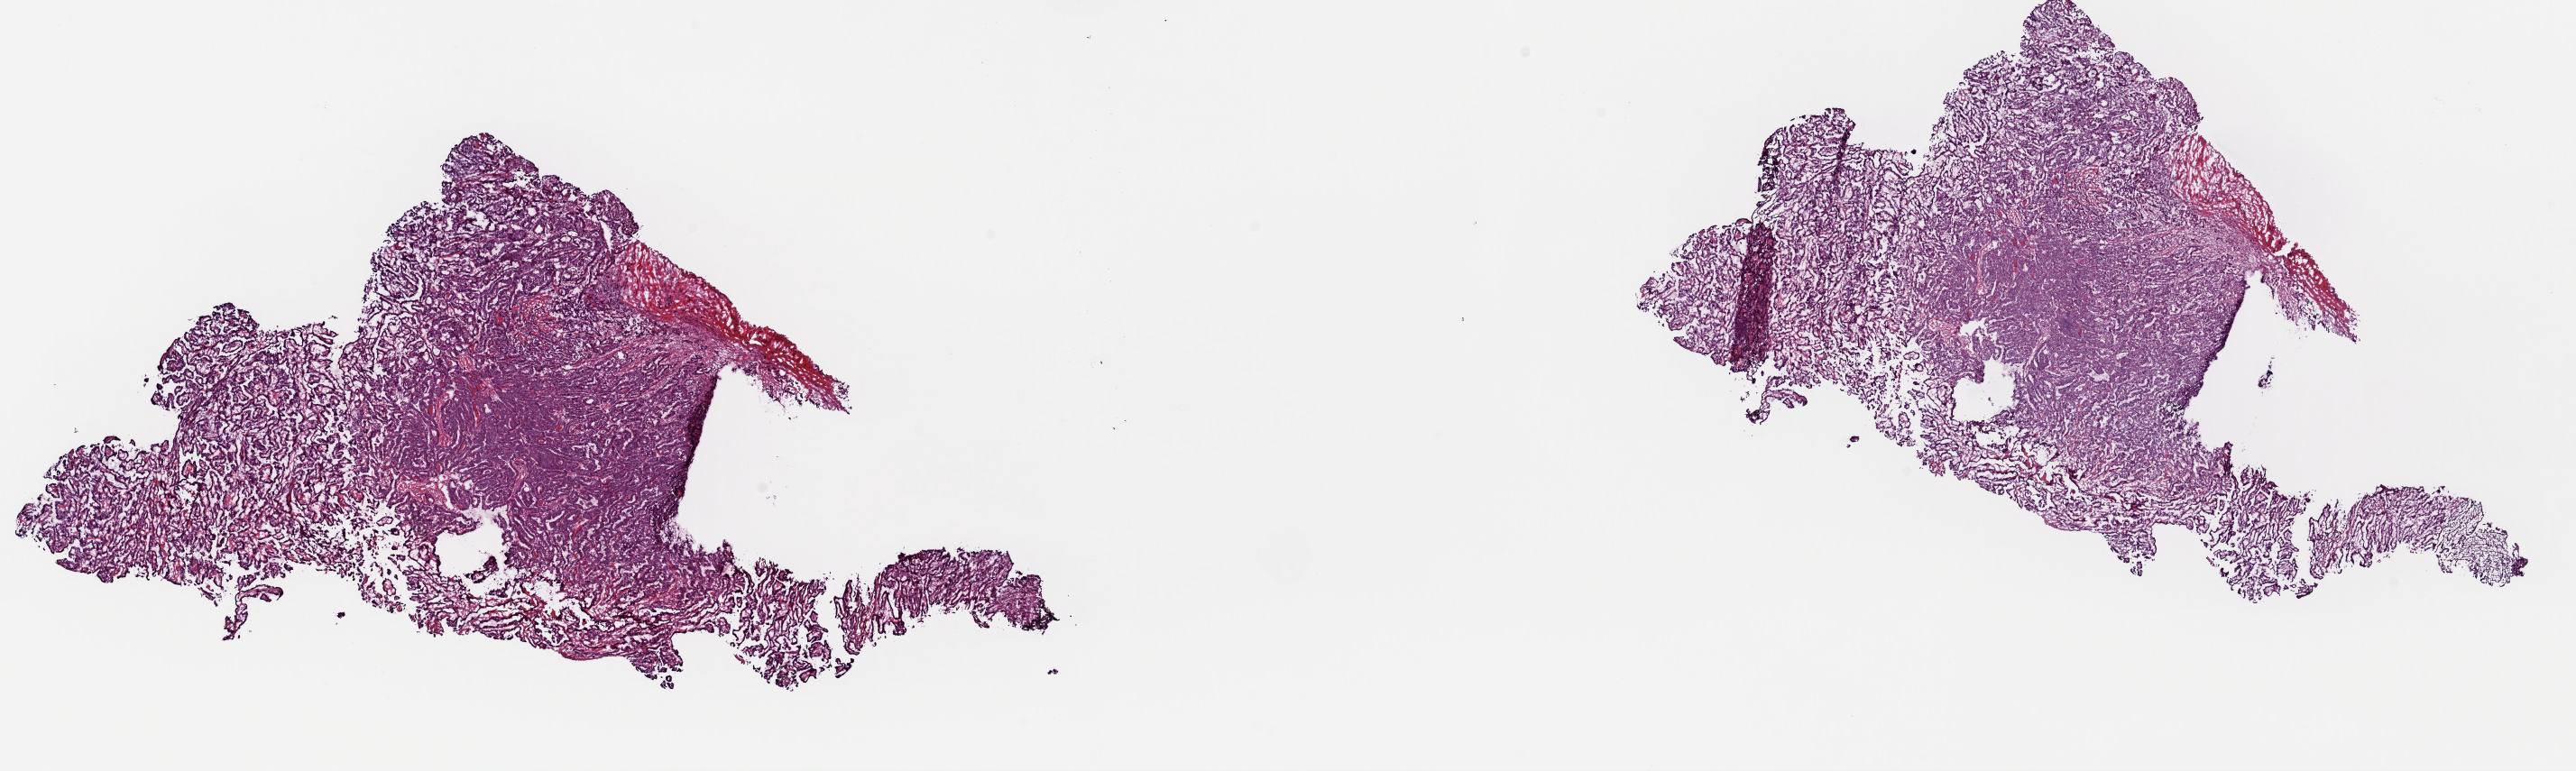
Hematoxylin and eosin (H&E) stained whole-slide image — a low-resolution overview of the entire scanned area, about 22.6 x 6.8 mm (acquisition: 40x scan), frozen section, primary tumour sample from the thyroid. Patient: female, age at initial diagnosis 61 years. Slide review estimates, as recorded: tumour cells 98%, tumour nuclei 95%, normal cells 0%, stromal cells 2%, necrosis 0%. Infiltration values recorded for this section: lymphocyte infiltration 0%, monocyte infiltration 0%, neutrophil infiltration 0%.
• AJCC pathologic stage: IVA (6th edition)
• histologic diagnosis: Papillary carcinoma, follicular variant (thyroid gland)
• lymph nodes positive (case pathology): 5 of 6 examined